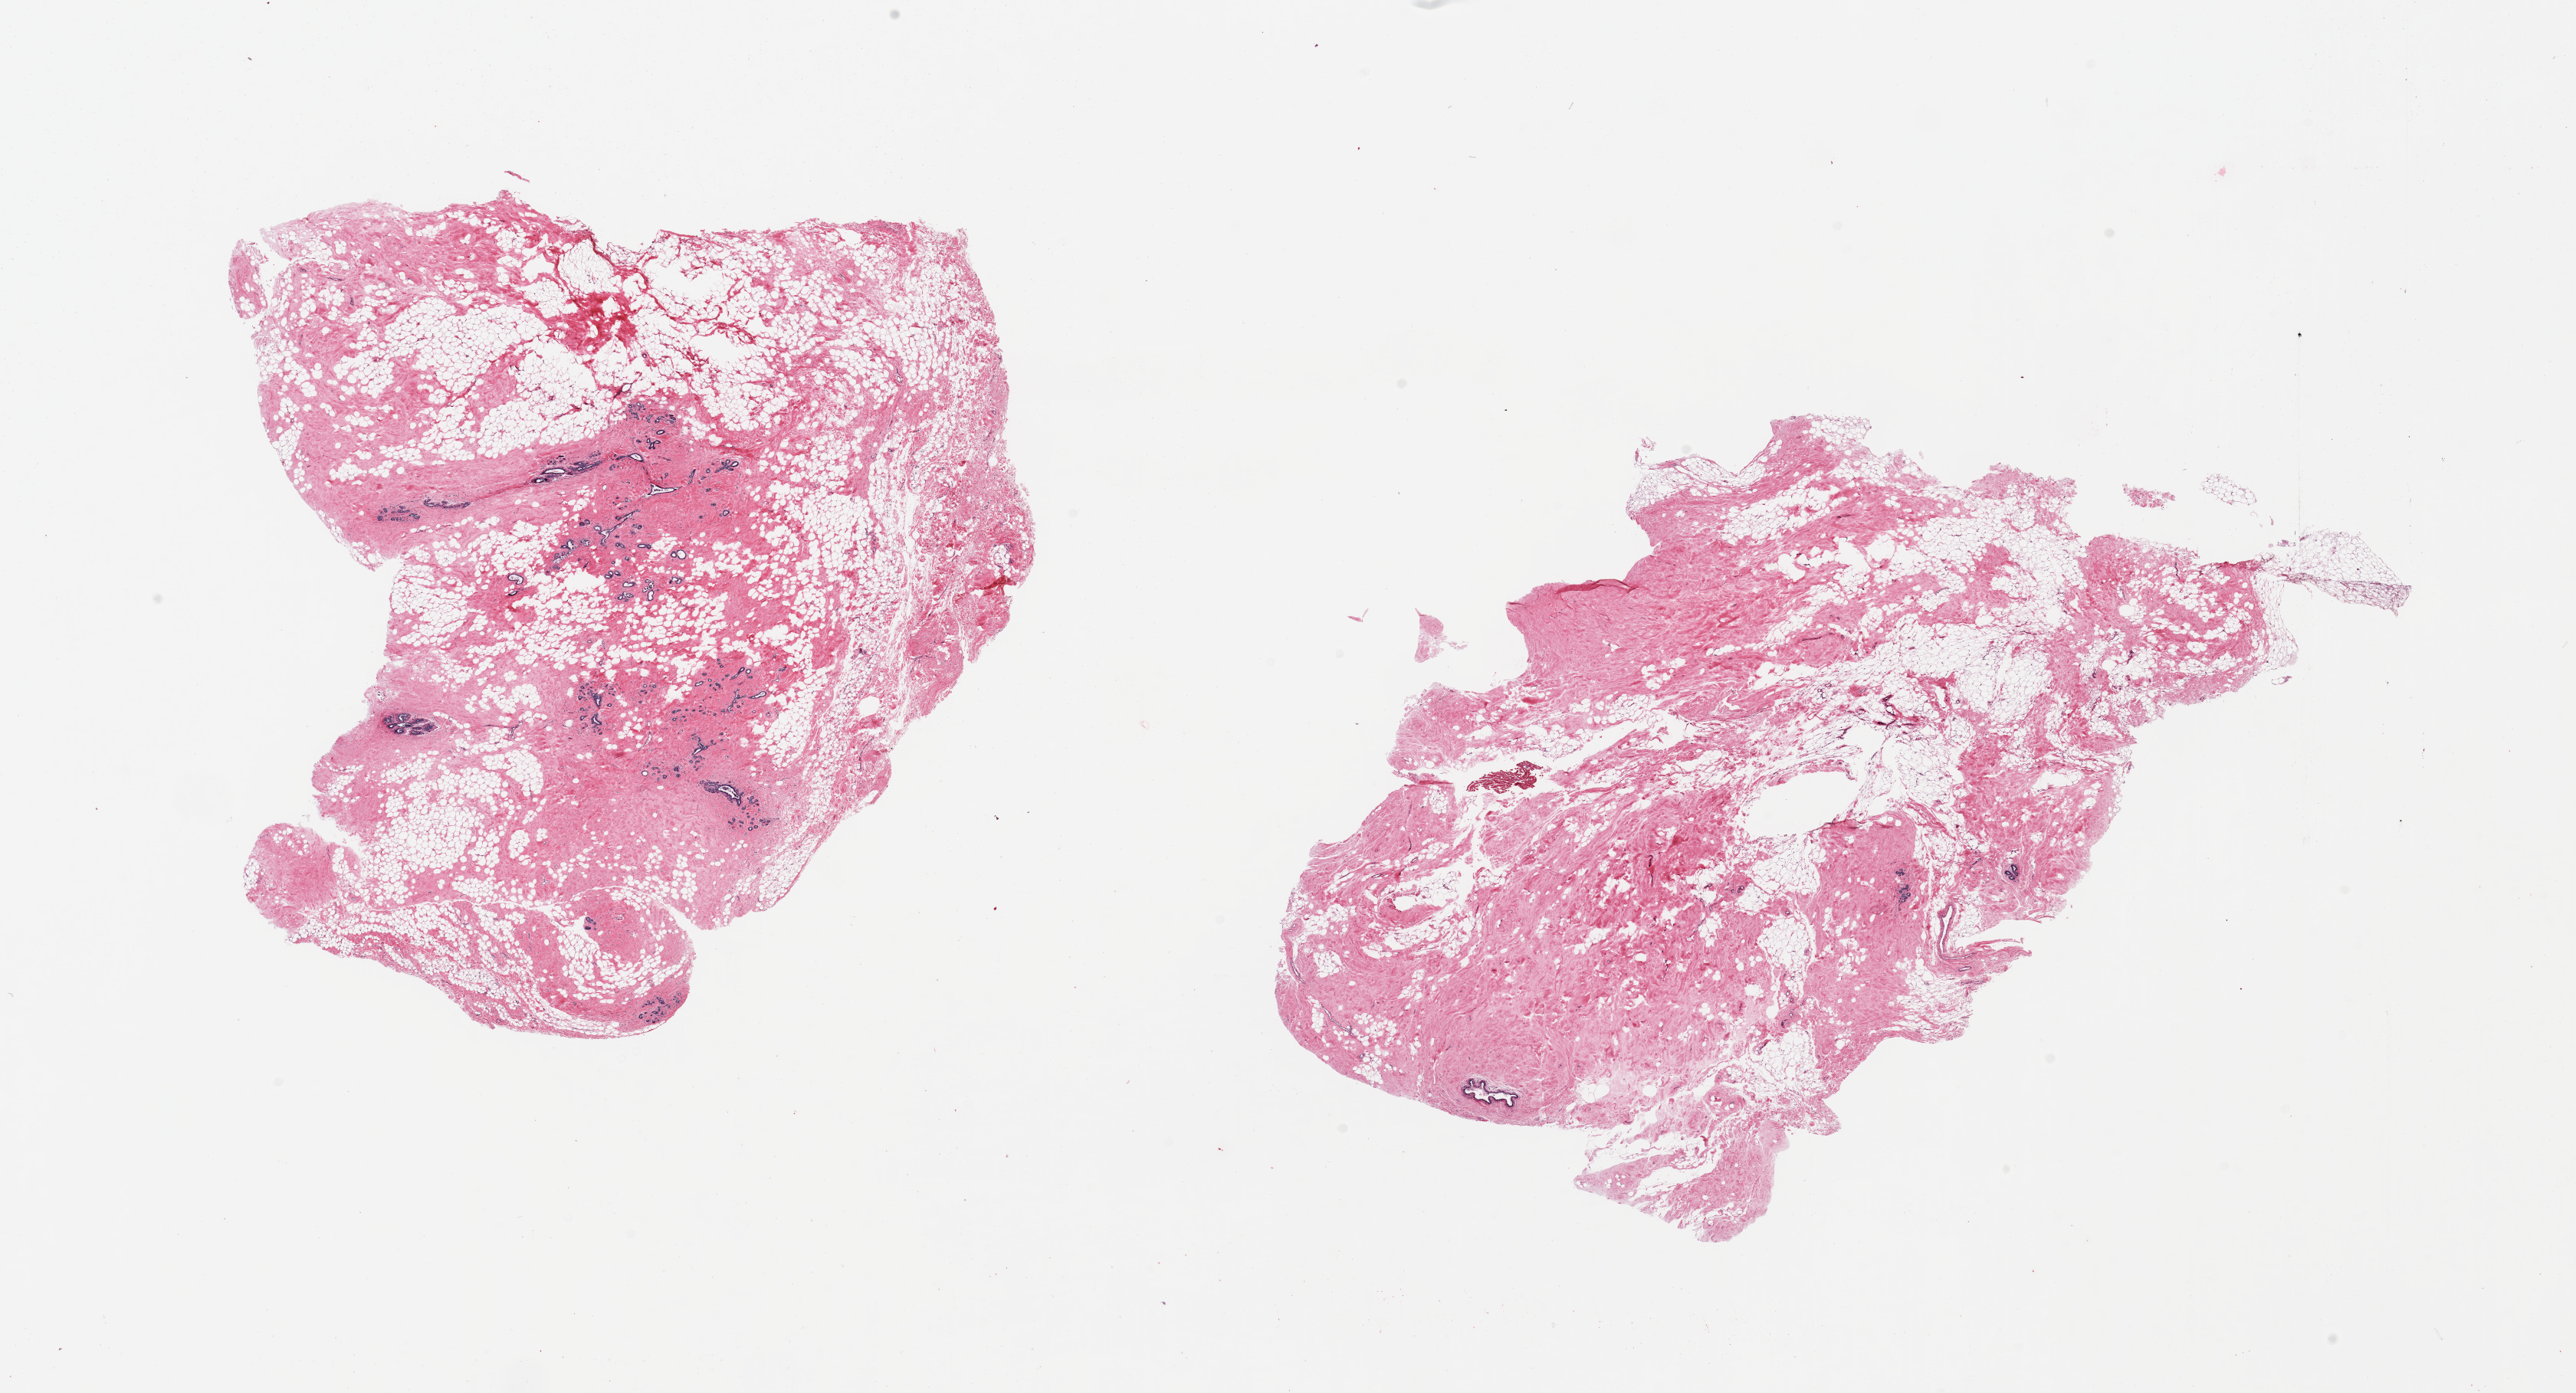
Whole-slide image, haematoxylin and eosin stain, brightfield, whole scanned area (about 26.6 x 14.4 mm, acquisition: 20x scan) shown as a low-resolution overview, PAXgene-fixed paraffin-embedded (PFPE) section, sampled site (target tissue): breast, tissue donor sample.
Reviewer comment on this tissue sample: 2 pieces, atrophic ductal lobular units present, rep.